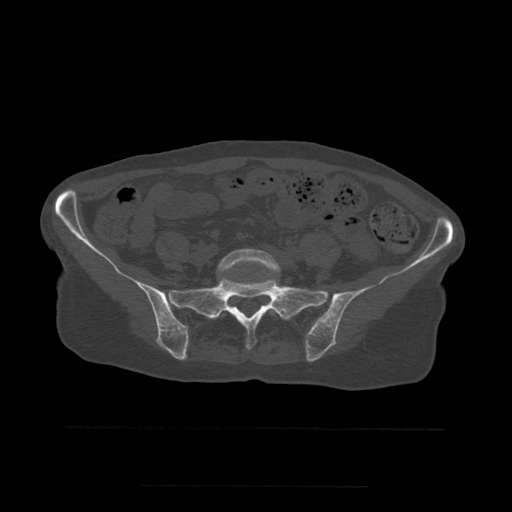
CT including the spine, one axial slice; position 132 of 544 along the scan axis; bone window (W 1800 / L 400 HU); 1.25 mm slice thickness; 512 × 512 image matrix, field of view 350 × 350 mm. Patient age 58 years. Case-level facts recorded for this patient, not image findings: primary cancer: lung.
Outlined on this slice (semi-automatically segmented with operator editing):
- L5 vertebra: bounding box [x1, y1, x2, y2] px = [218, 249, 281, 317]